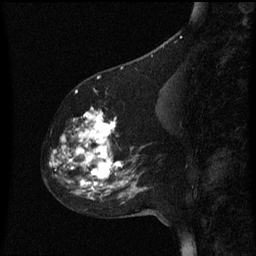
Breast MRI (dynamic contrast-enhanced), one sagittal slice; position 25 of 60 along the scan axis; dynamic contrast-enhanced series, image 2 of 3 at this slice position (ordered by acquisition); 1.5 T; TE 4.2 ms, TR 8 ms; 2 mm slice thickness; 256 × 256 image matrix. Patient: female, 60 years.
Structures marked on this image (semi-automatically segmented with operator editing):
- analysis volume of interest (the breast-tissue region the enhancement analysis was run in; not a lesion): bounding box (x1, y1, x2, y2) in pixels: (49, 108, 158, 197)
- tumour enhancement mask (voxels above the 70 % enhancement threshold inside the analysis volume of interest): (51, 108, 129, 197)